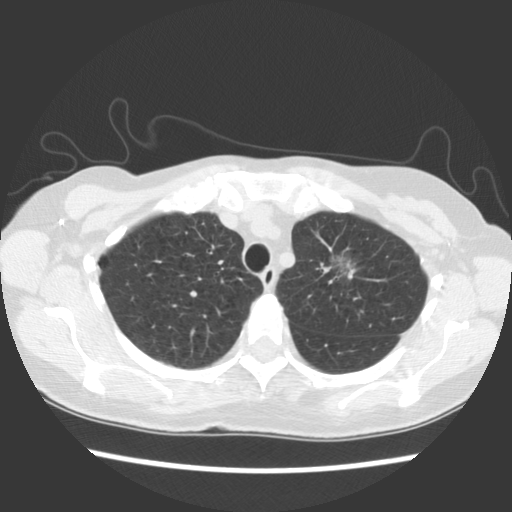
Chest CT (low-dose screening protocol), one axial image; first (baseline) screen; lung window (W 1500 / L -600 HU); 140 kVp; slice 98 of 129 in the series; 512 × 512 image matrix, field of view 325 × 325 mm. Female participant, aged 65 years at enrolment. Former smoker at enrolment.
Expert reader's lesion annotation, bounding box [x1, y1, x2, y2] px = [312, 237, 380, 297]. Screening reader's record for this exam (one nodule recorded; not confirmed to be the boxed lesion): non-calcified nodule or mass ≥4 mm, left upper lobe, 11 × 10 mm, poorly defined margins, ground glass attenuation.